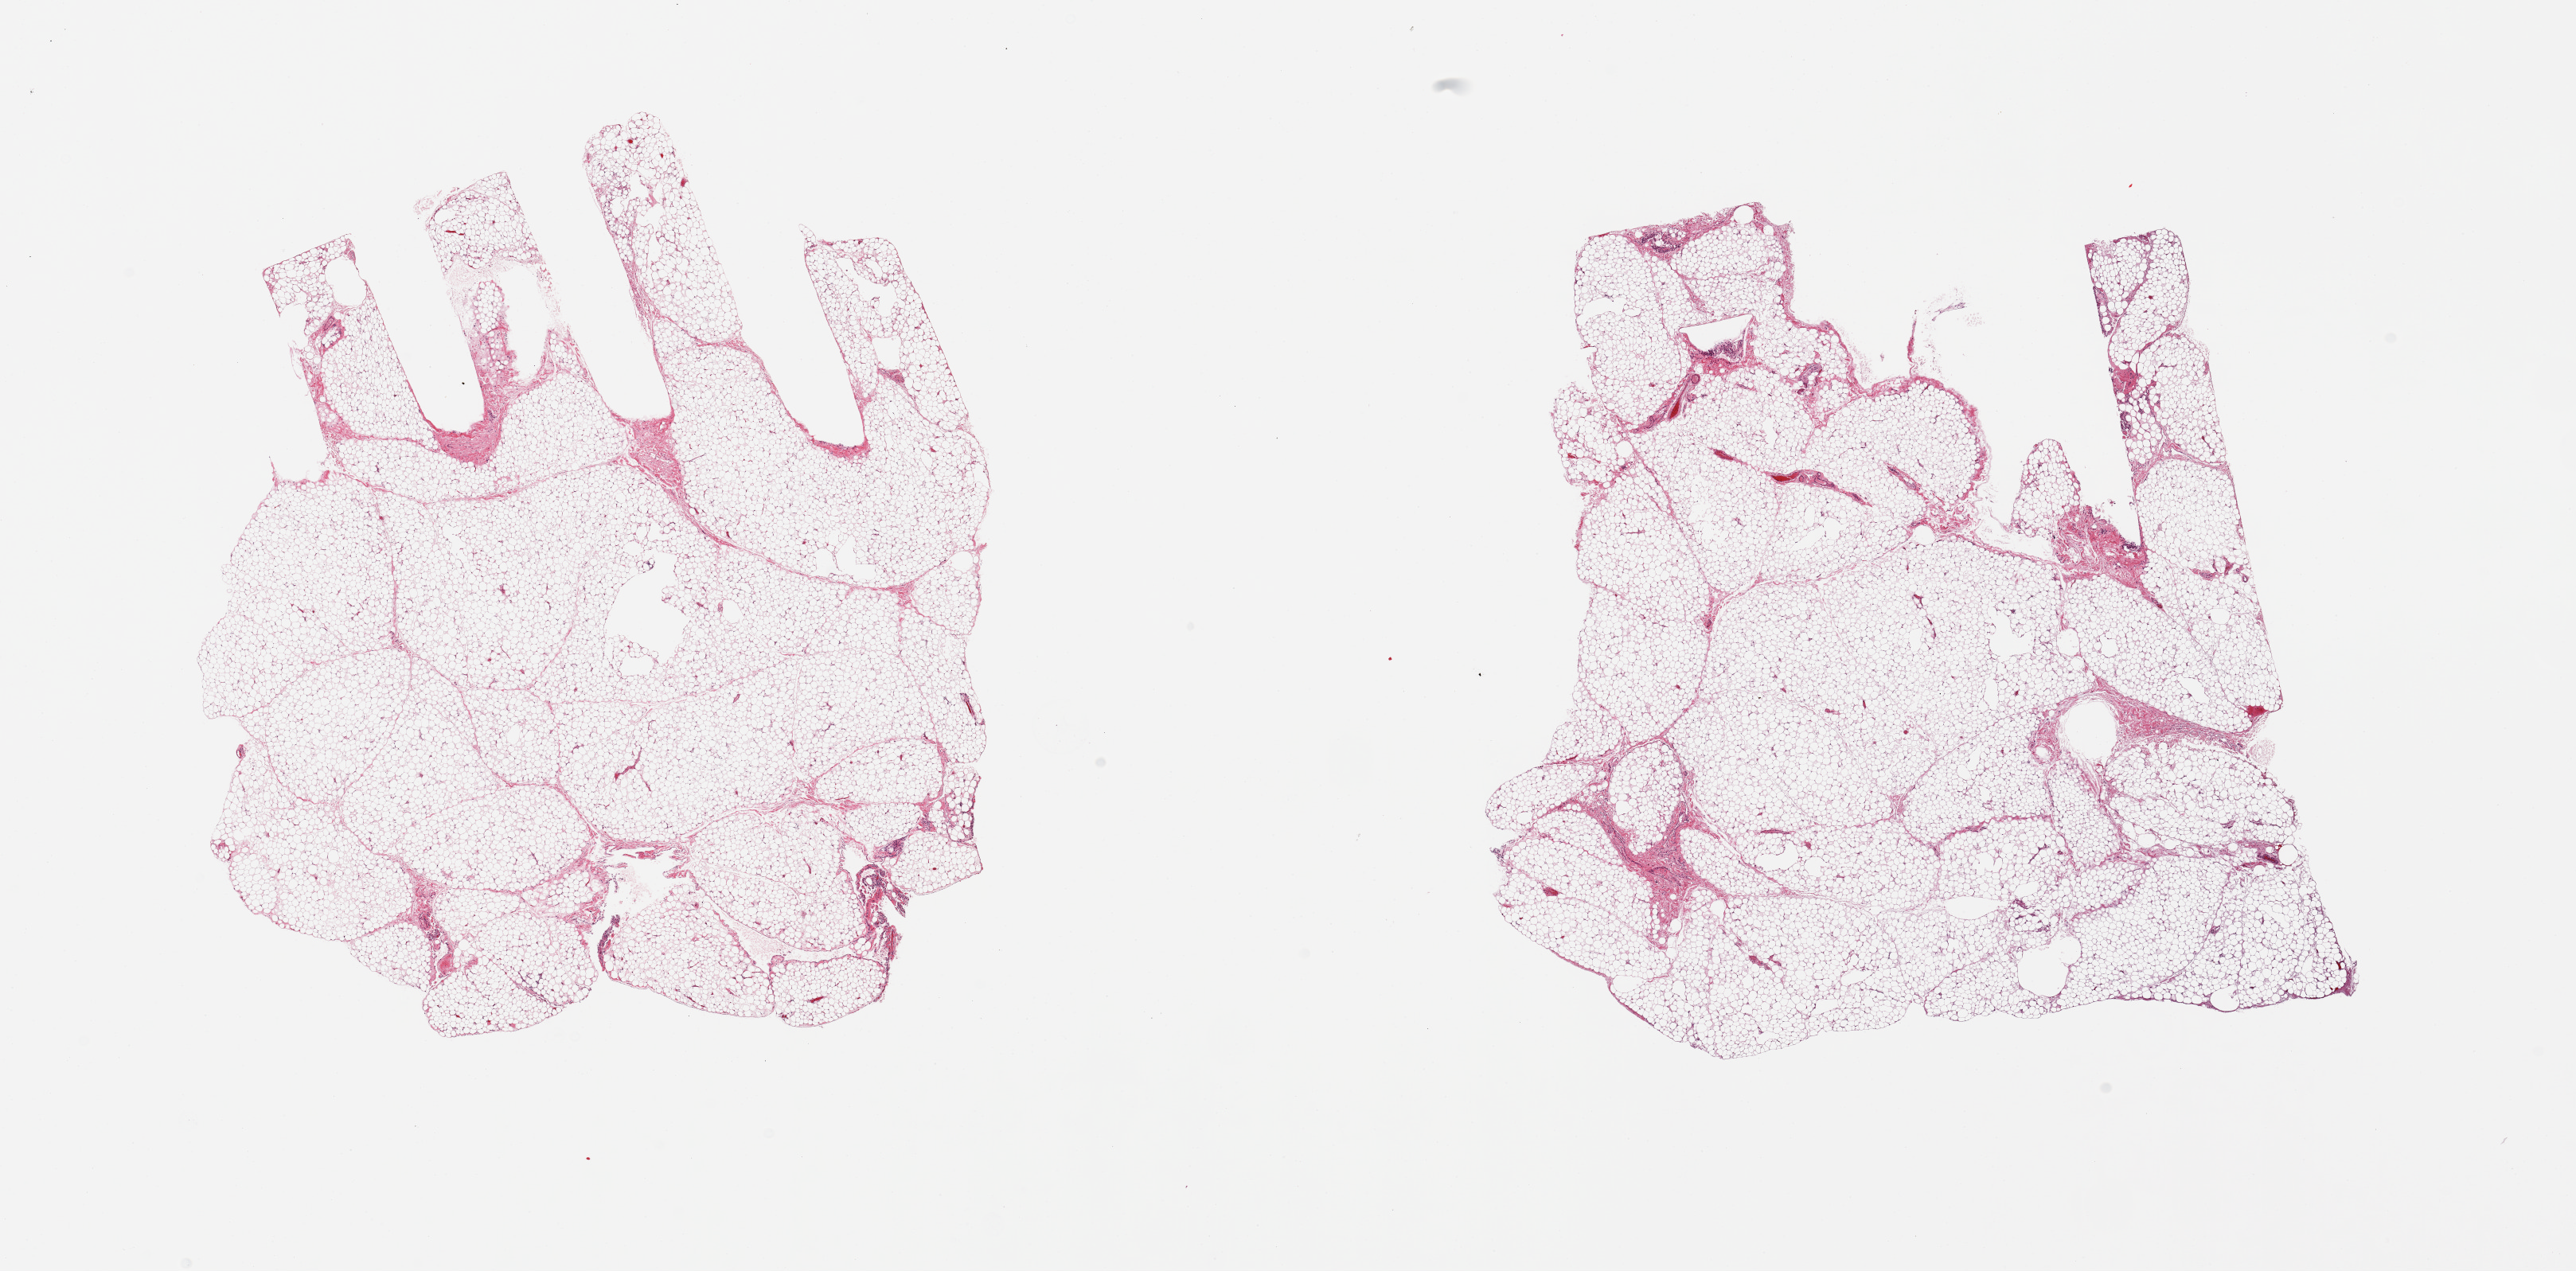
Whole-slide image, hematoxylin and eosin (H&E) stain, shown as a low-resolution overview of the whole scanned area (about 25.6 x 12.6 mm, acquisition: 20x scan), PAXgene-fixed, paraffin-embedded tissue, target tissue: omentum, tissue donor sample. Donor sex: male.
Review note (as recorded): 2 pieces.